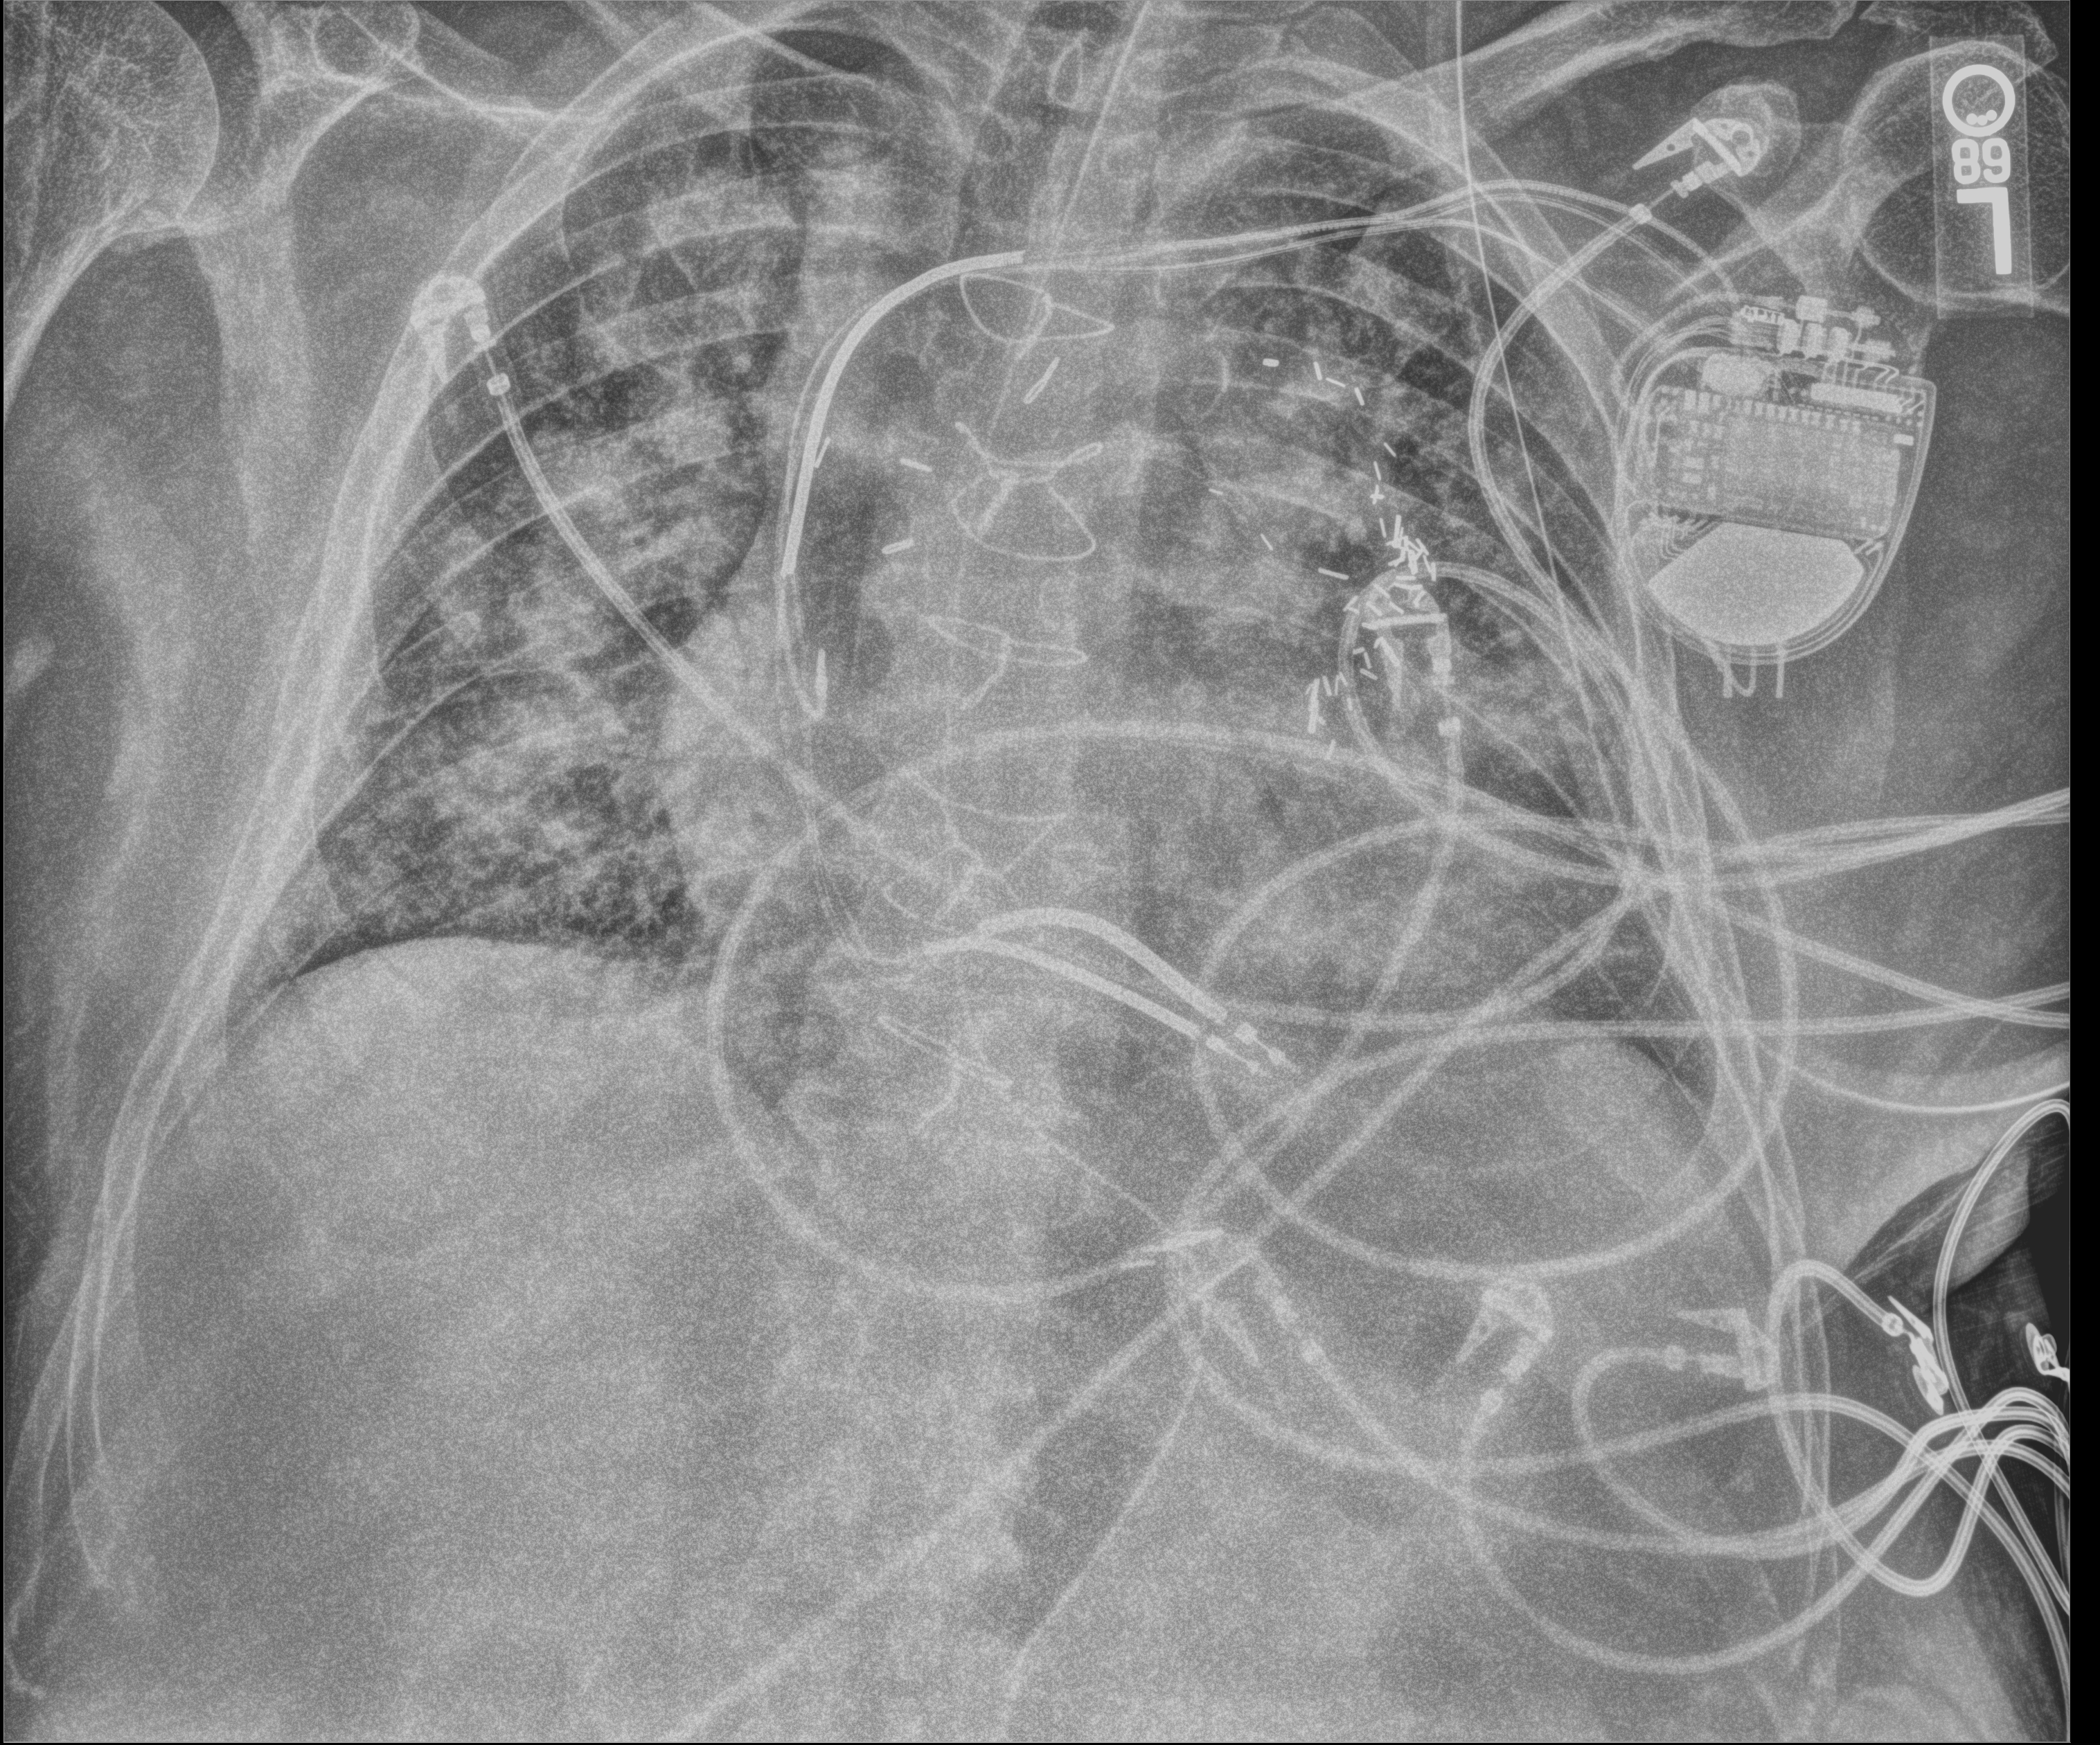
Portable chest radiograph, anteroposterior (AP) projection. Male patient hospitalised with COVID-19, age 60–74 years.
Hospital-stay facts (about this admission, not read from this image; timing relative to this image not recorded):
- admitted to intensive care during this hospital stay: yes